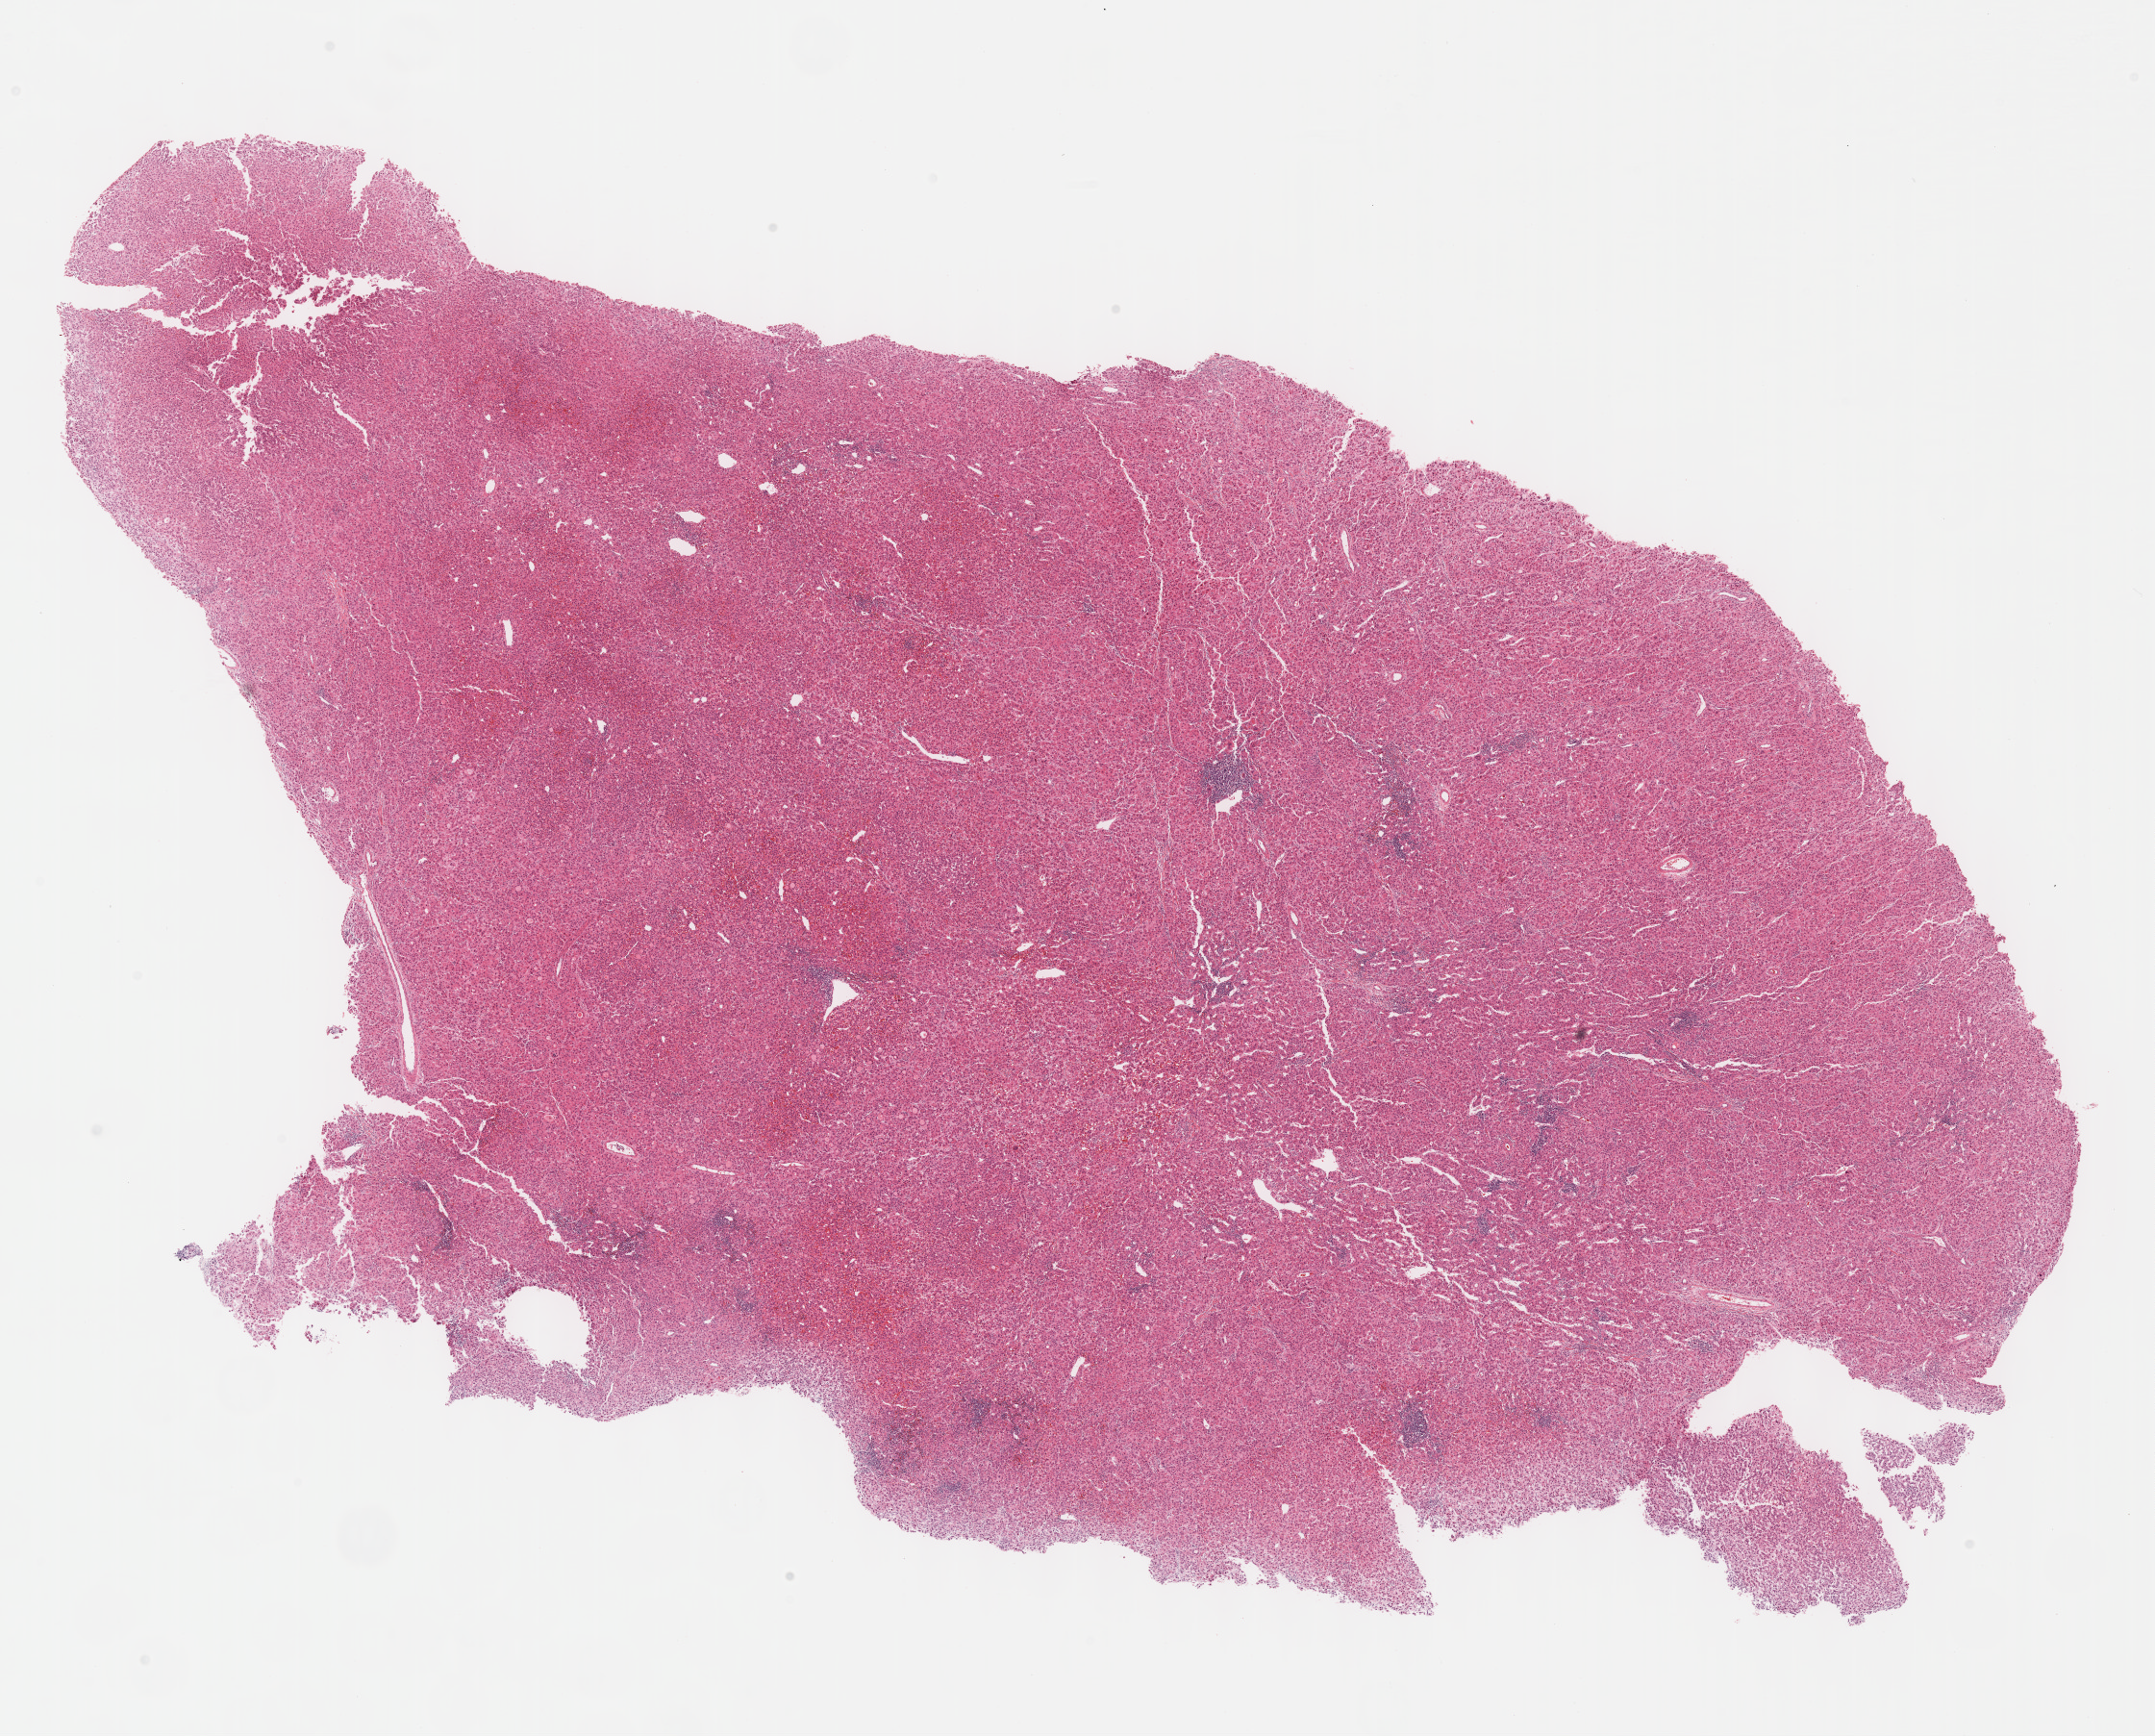
Whole-slide histology image, H&E-stained, whole scanned area (about 18.1 x 14.6 mm, slide scanned at 40x) shown as a low-resolution overview, FFPE section, primary tumour sample from the liver. Female patient; age at initial diagnosis 66 years. Histologic grade: G3 (poorly differentiated).
- AJCC pathologic stage: I (7th edition)
- diagnosis: Hepatocellular carcinoma, NOS